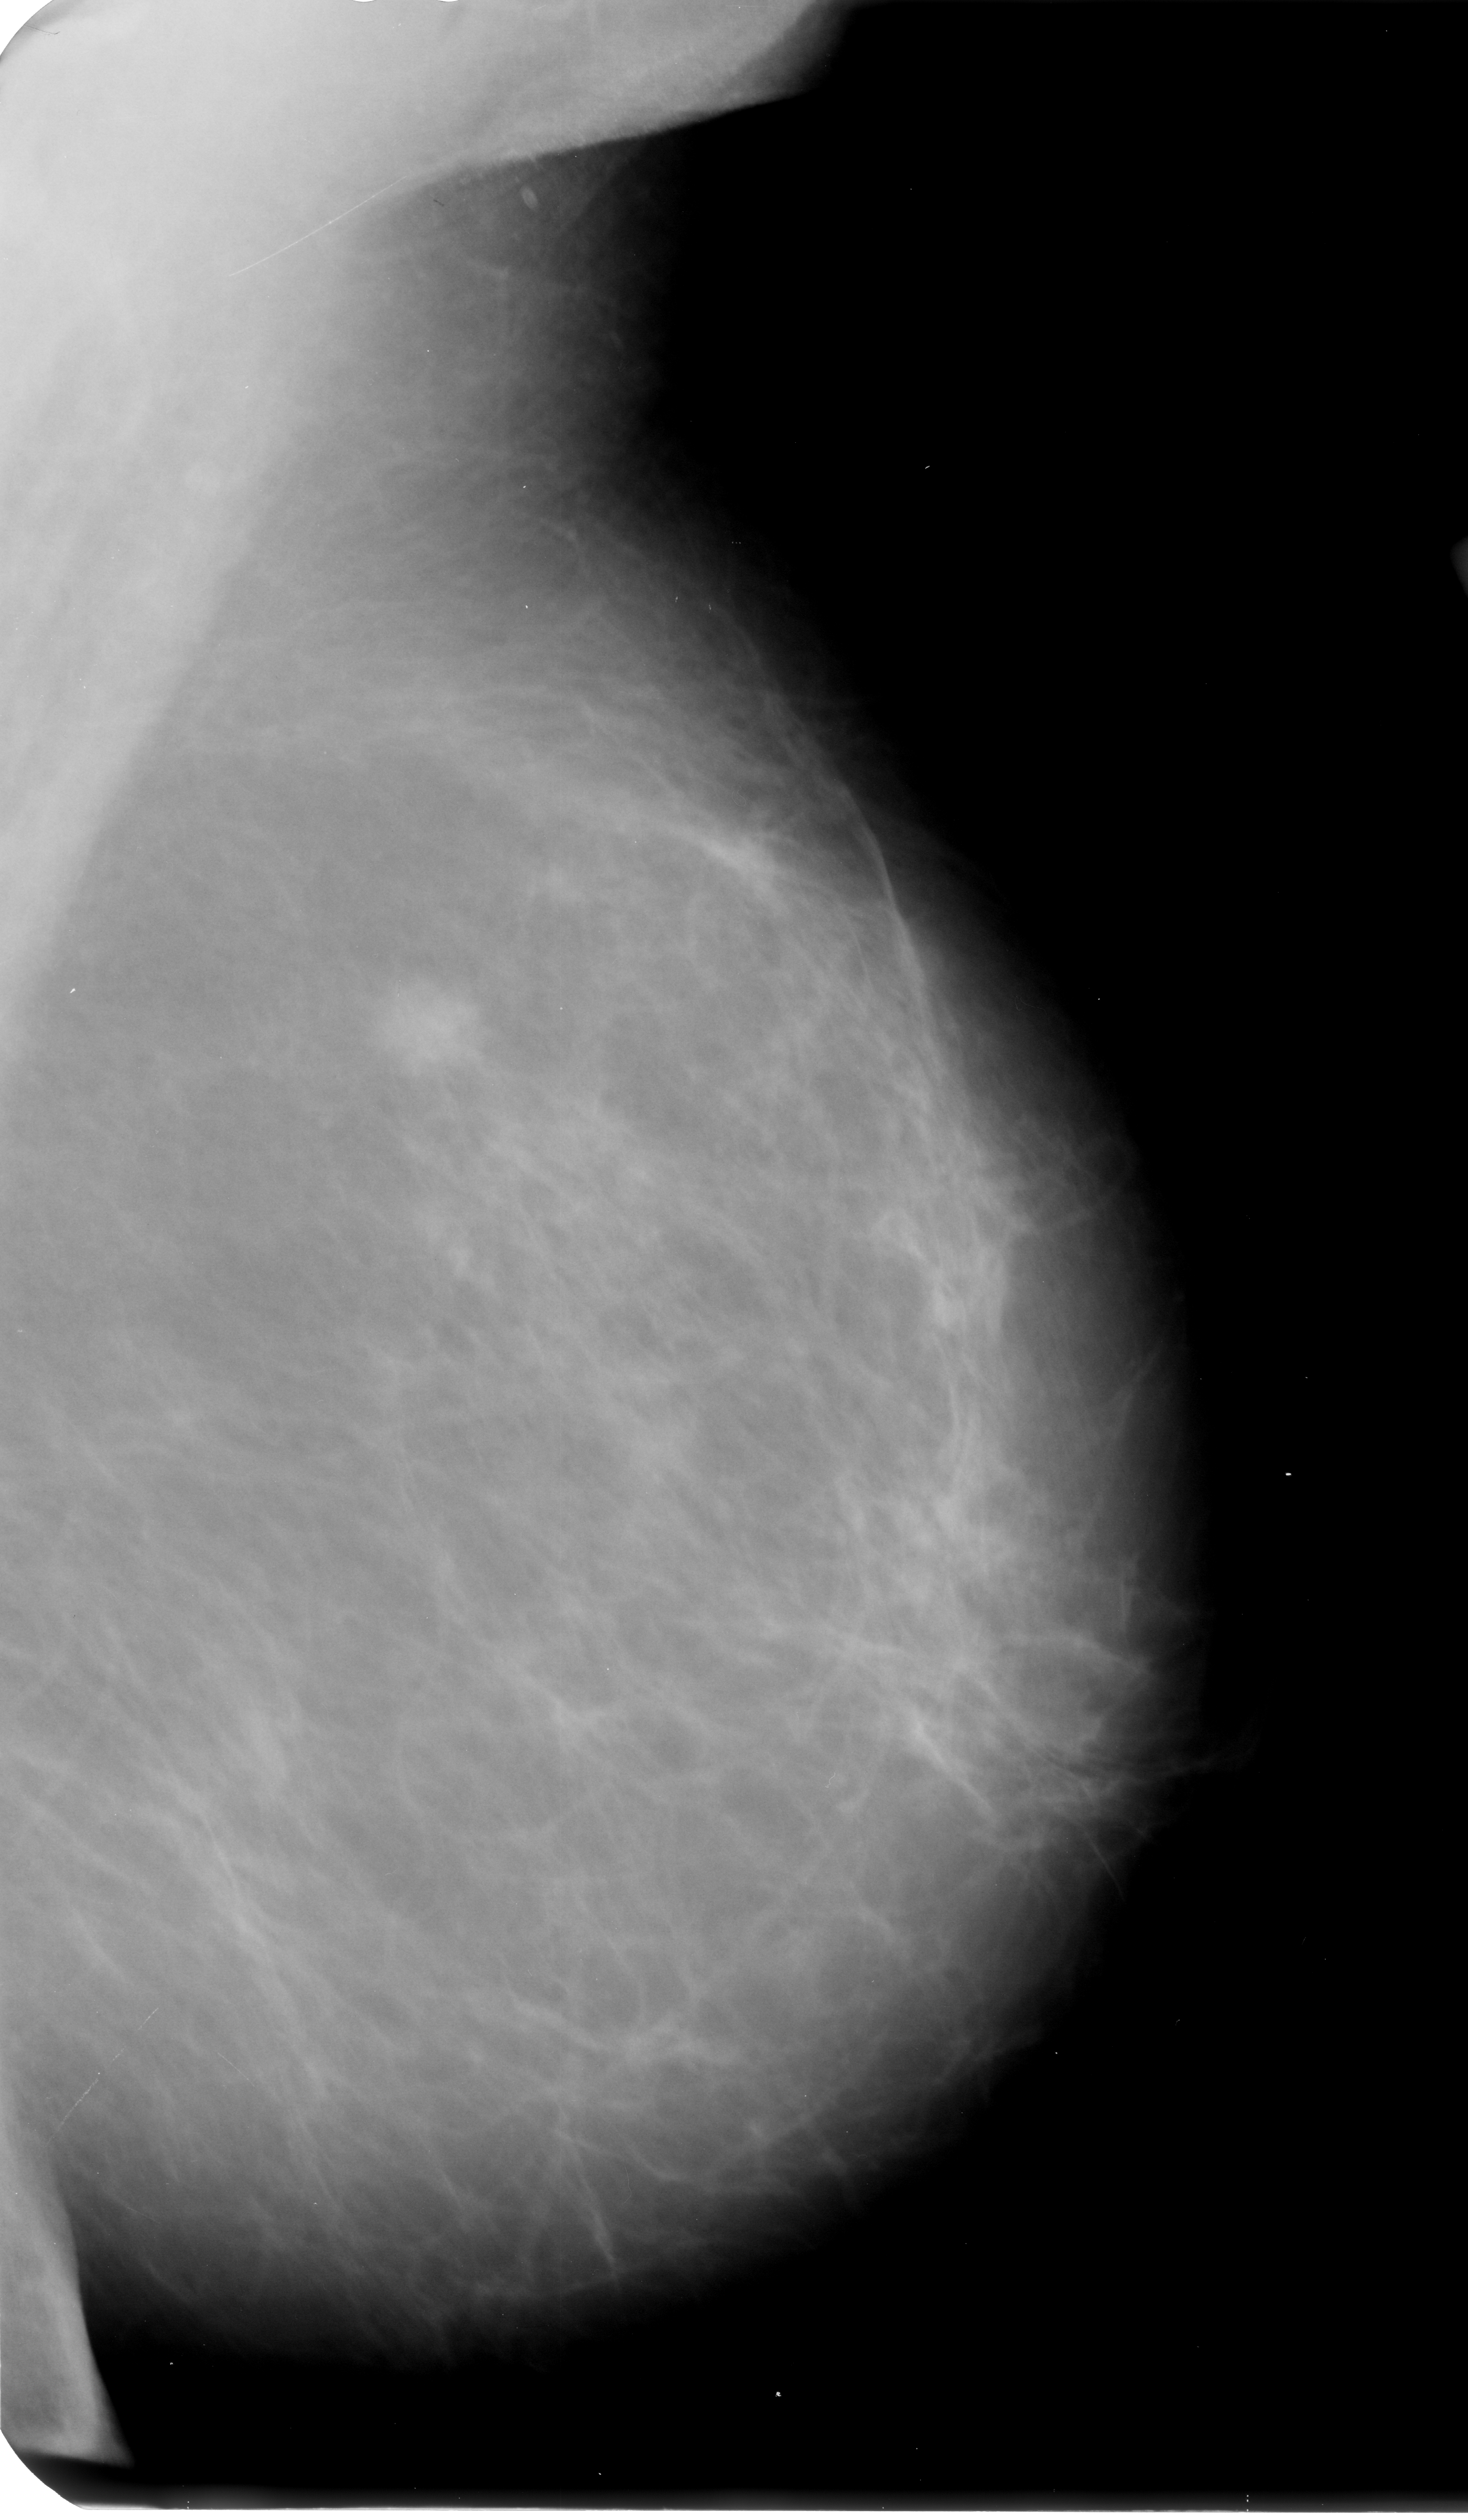
Mammogram (digitized film); left breast; mediolateral oblique (MLO) view; 1468 × 2520 image matrix.
Marked abnormalities (boxes around the expert regions of interest):
- mass, shape irregular, margins spiculated; BI-RADS assessment category 4; pathology result (as recorded, not read from the image): malignant: bounding box (x1, y1, x2, y2) in pixels: (373, 972, 492, 1082)